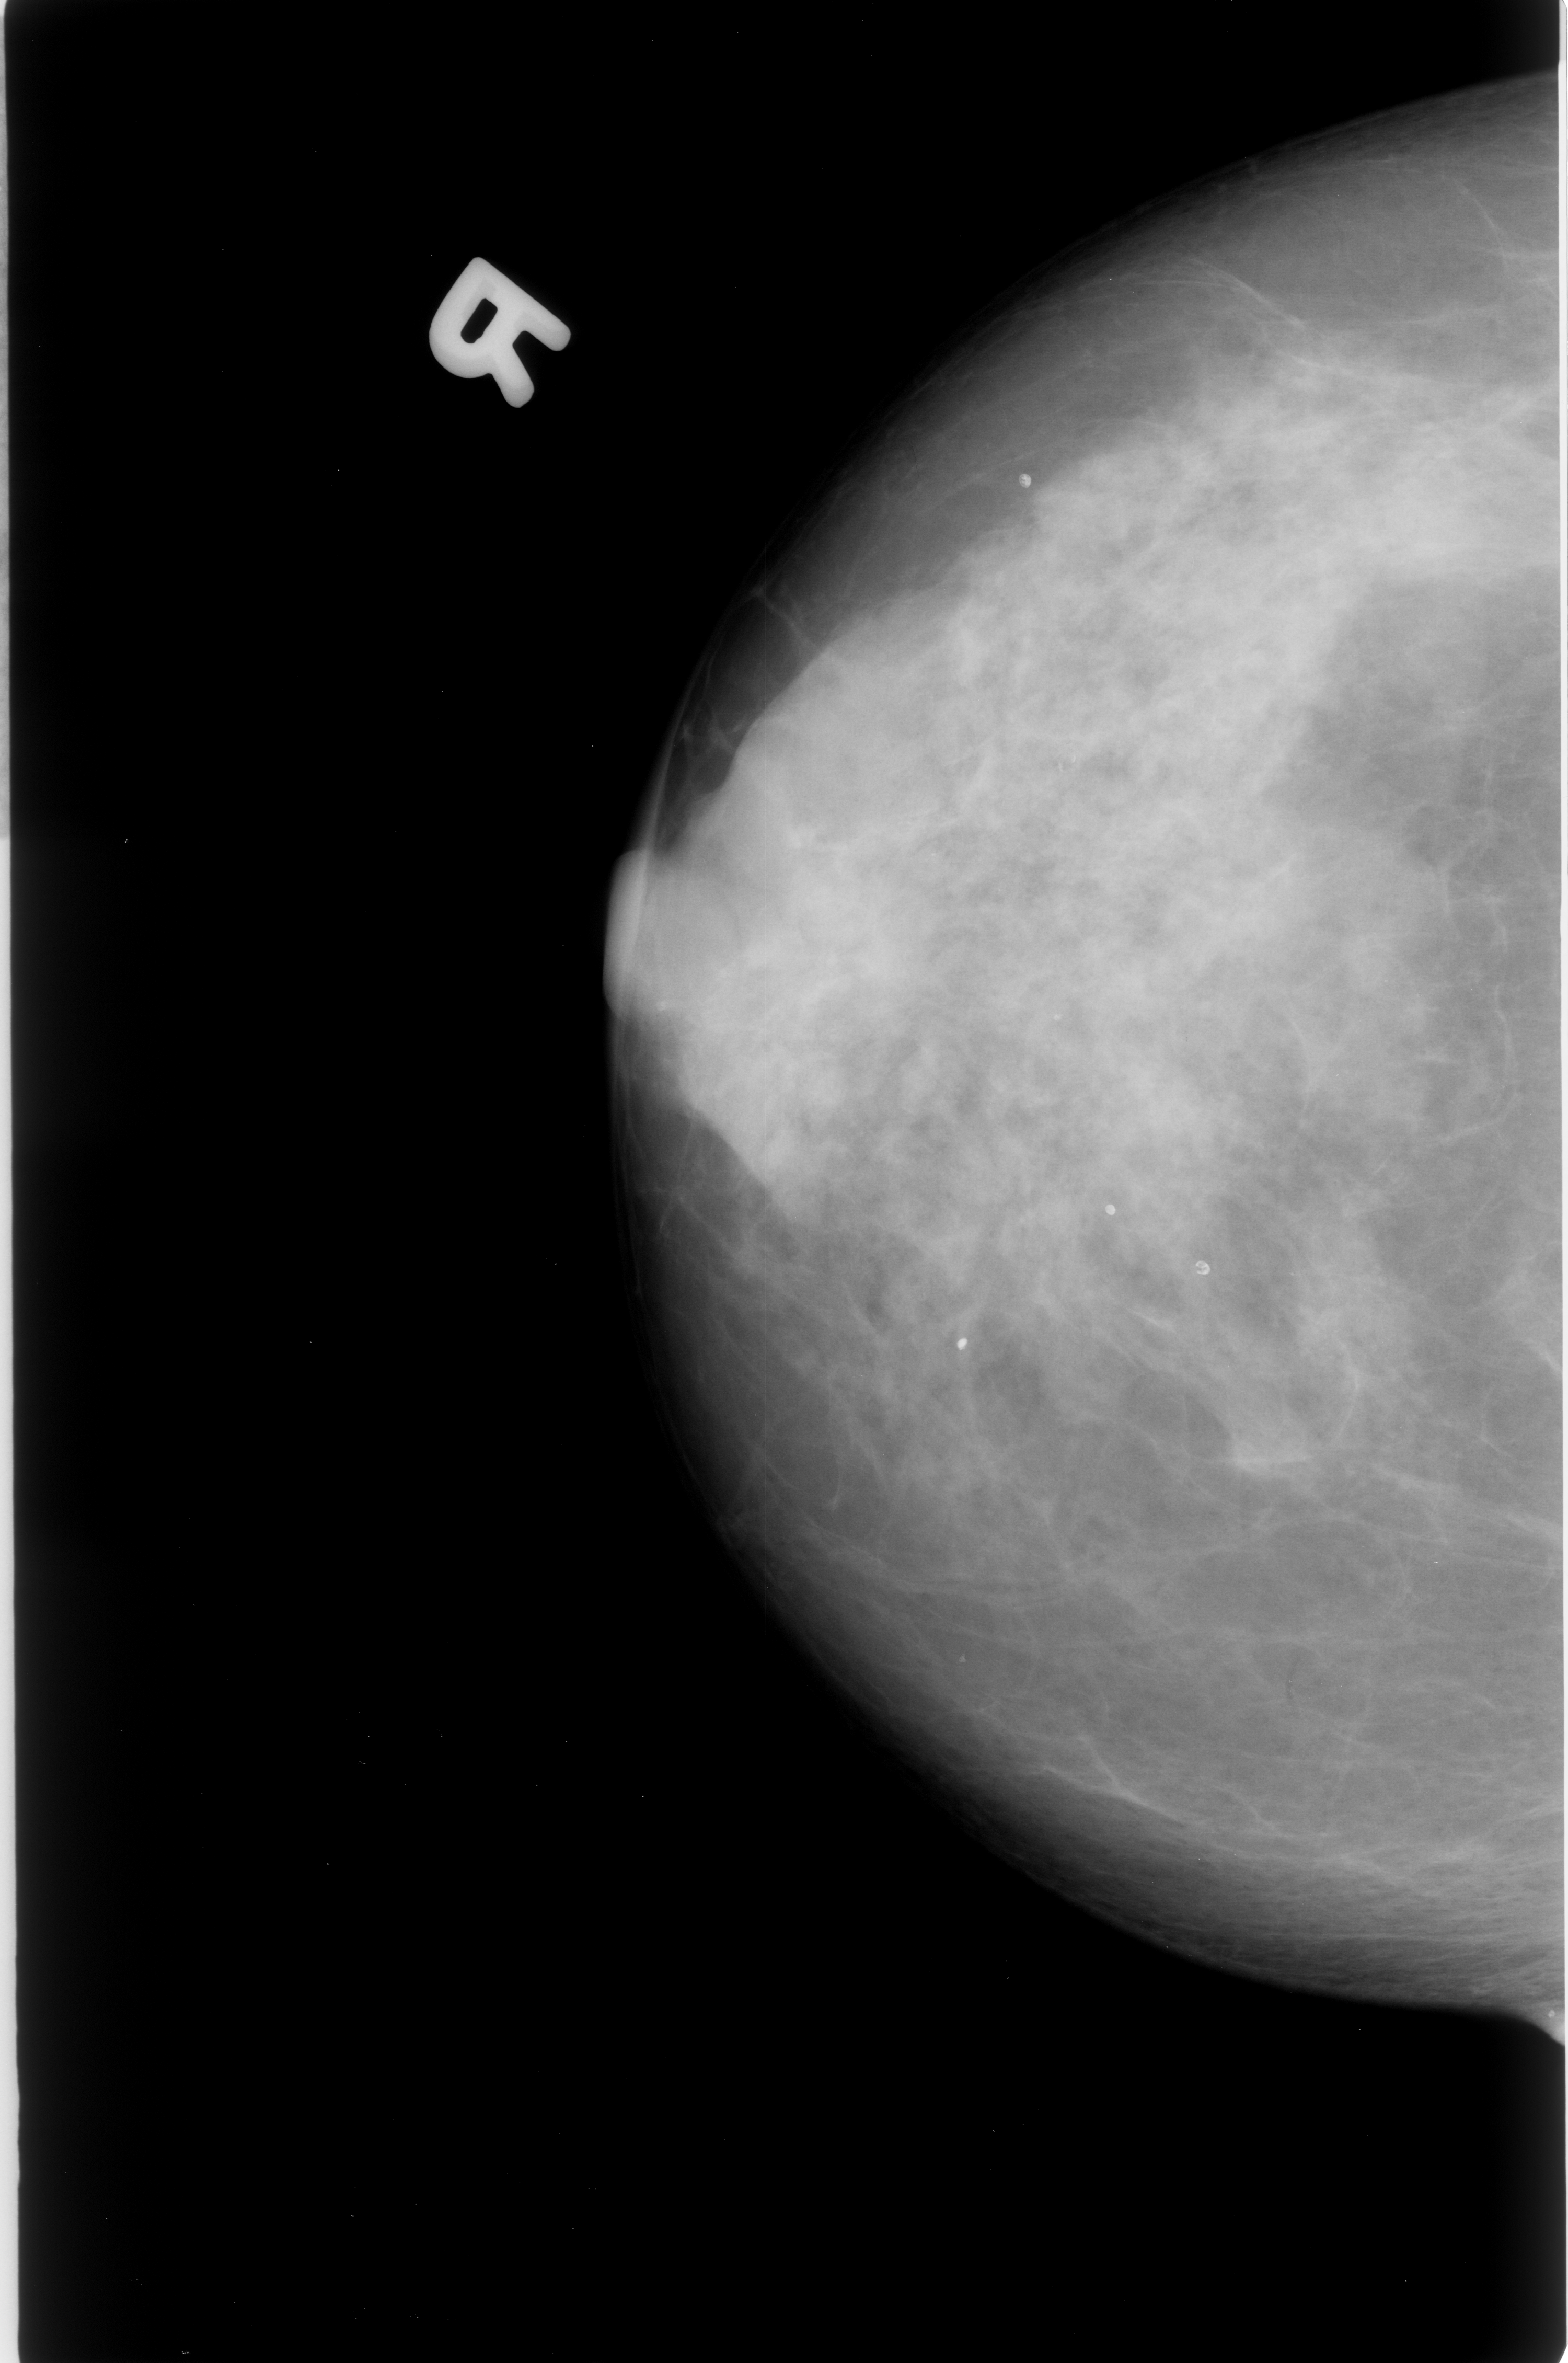
Mammogram (digitized film). Right breast. CC view. BI-RADS breast density category 3 (scale 1–4). 1568 × 2363 image matrix.
Marked abnormalities (boxes around the expert regions of interest):
- Finding 1 of 2: calcifications, morphology punctate / pleomorphic, distribution clustered; BI-RADS assessment category 3; subtlety rating 2 on a 1 (subtle) to 5 (obvious) scale; pathology (as recorded): malignant: box from (x=915, y=832) to (x=963, y=888) px
- Finding 2 of 2: calcifications, morphology punctate / pleomorphic, distribution clustered; BI-RADS assessment category 3; pathology (as recorded): malignant: (x=1045, y=731)–(x=1101, y=796)